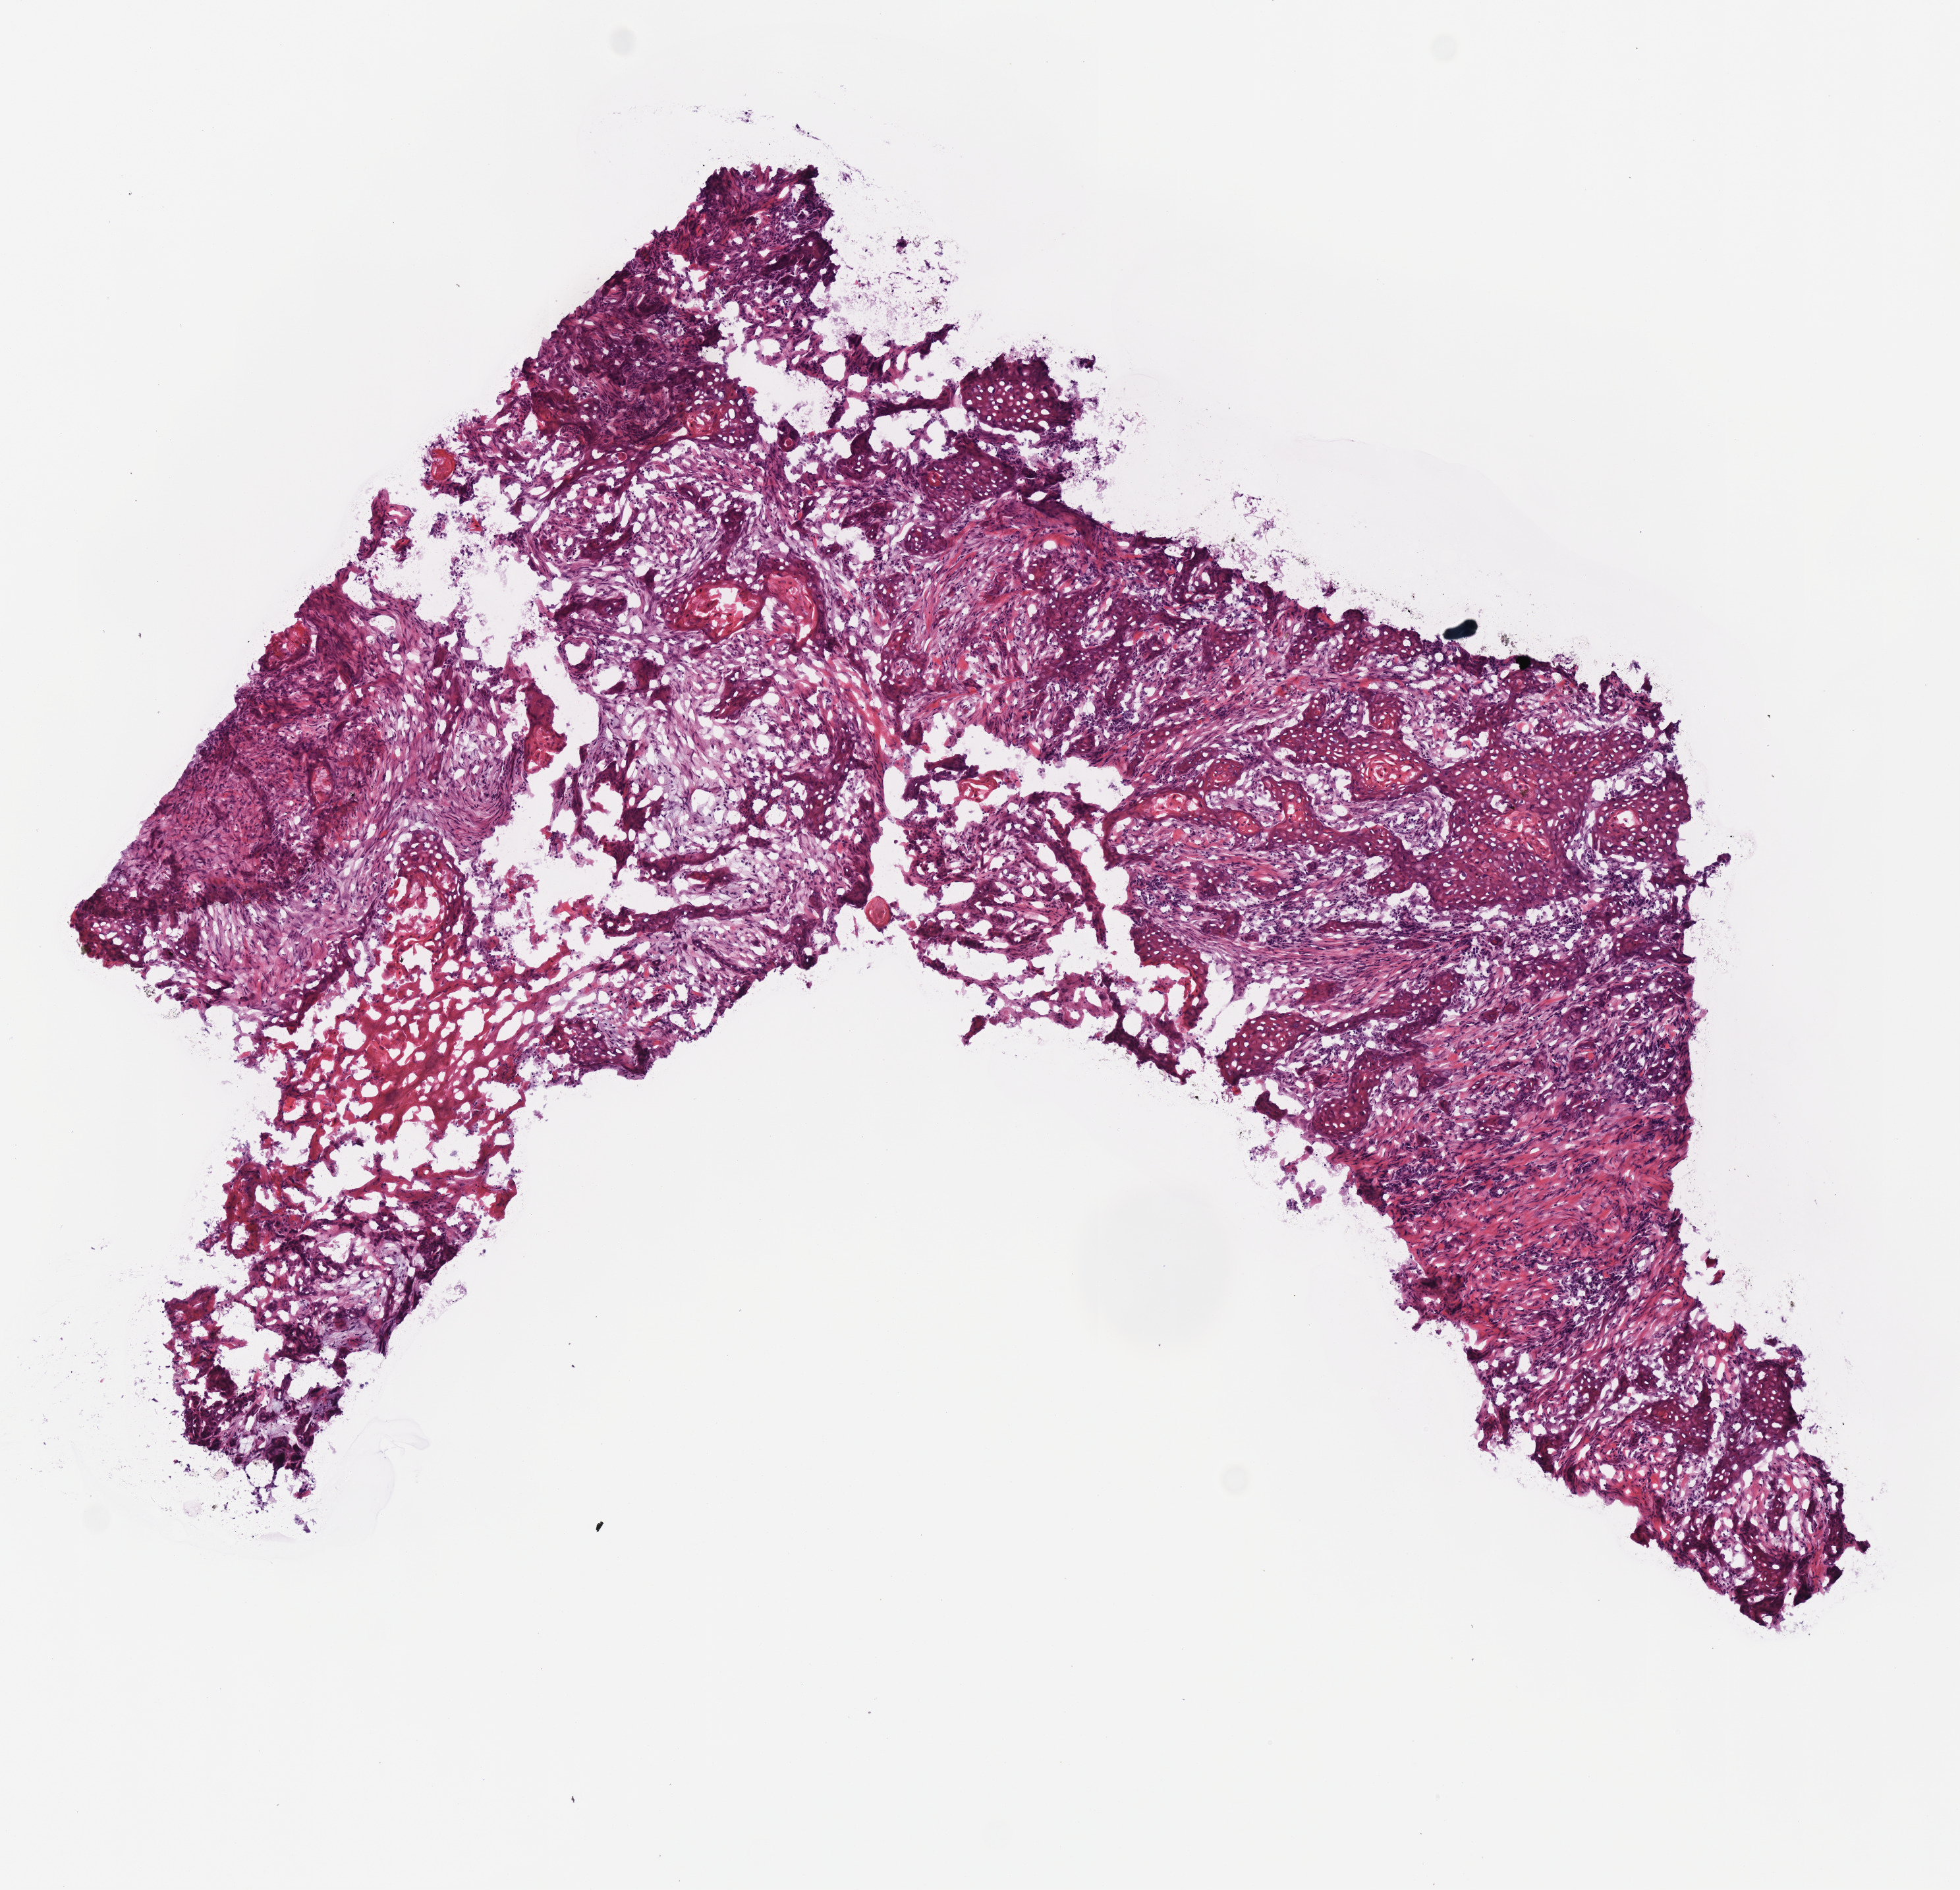
Digitized Hematoxylin and eosin (H&E) stained tissue section (whole slide) — a low-resolution overview of the entire scanned area, about 5.9 x 5.6 mm. Frozen section from the bottom of the tissue portion. Primary tumour sample from the head and neck. Patient: male, age at initial diagnosis 60 years. Pathologist review of this section (percent, as recorded): tumour cells 80%, tumour nuclei 55%.
Pathologic diagnosis: Squamous cell carcinoma, NOS (larynx, NOS).